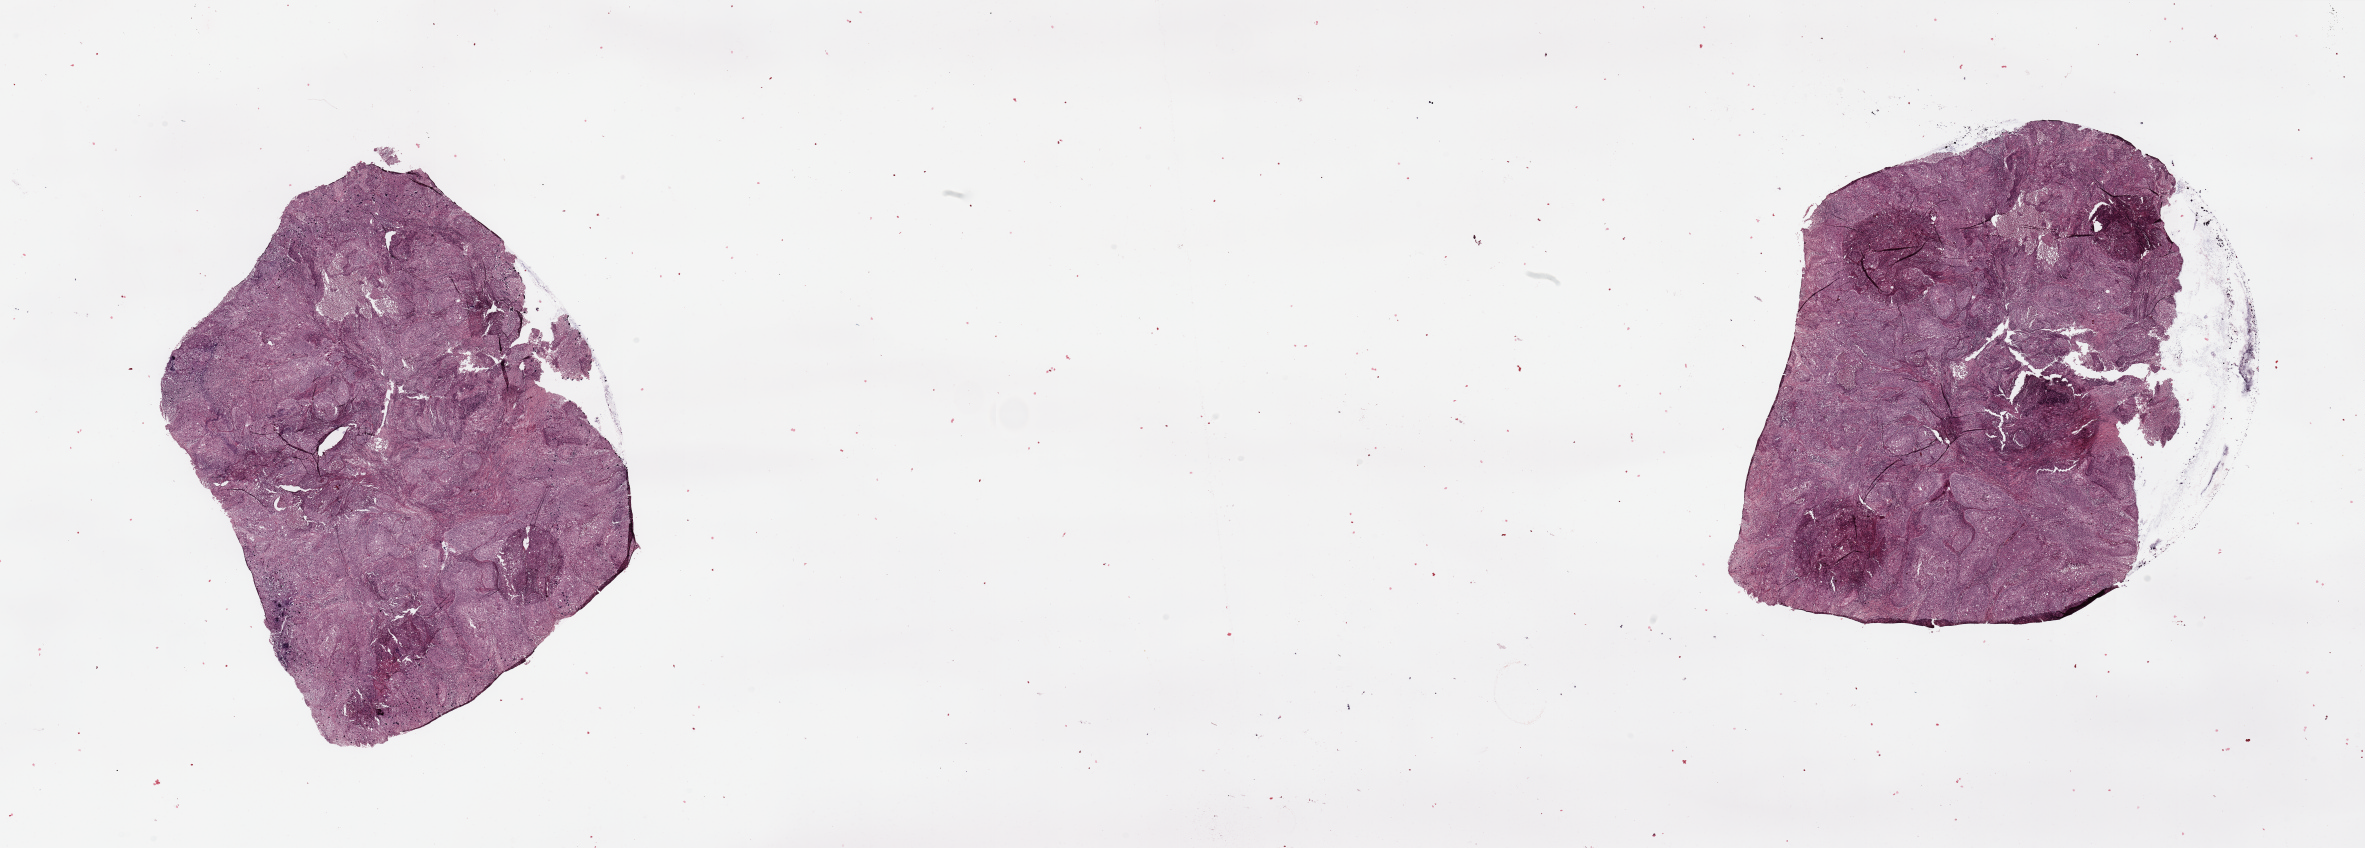
Digitized H&E tissue section (whole slide) — low-resolution overview of the scanned area, about 37.4 x 13.4 mm; lung, tumour tissue. Patient: male, age 68 years.
Patient diagnosis (cohort enrolment): squamous cell carcinoma (lung).